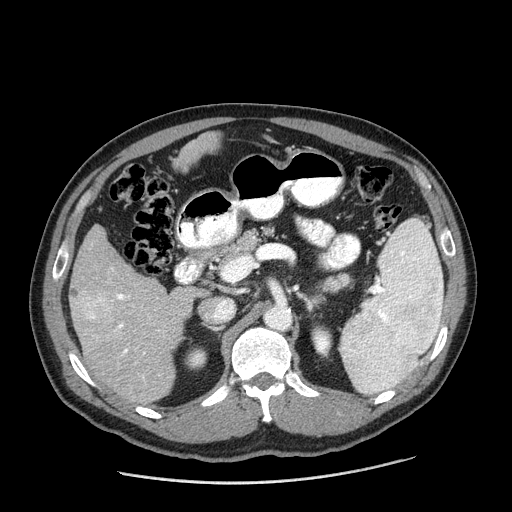
Contrast-enhanced abdominal CT (liver protocol), one axial slice. Position 93 of 198 along the scan axis. Reconstruction kernel STANDARD. One of 2 acquisitions stored at this slice position. Soft-tissue window (W 400 / L 40 HU). 2.5 mm slice thickness. 512 × 512 image matrix, field of view 400 × 400 mm. Case-level facts recorded for this patient, not image findings: diagnosis: hepatocellular carcinoma (patient treated with transarterial chemoembolisation; whether this scan precedes or follows treatment is not stated here); TNM stage (as recorded): Stage-II; Child-Pugh class: A.
Outlined on this slice (semi-automatically segmented with operator editing):
- liver parenchyma outside the tumour (the mass and vessels are separate outlines, so this box may not span the whole liver): bounding box (x1, y1, x2, y2) in pixels: (70, 132, 219, 402)
- mass: (67, 285, 115, 325)
- liver vessels: (111, 269, 145, 355)